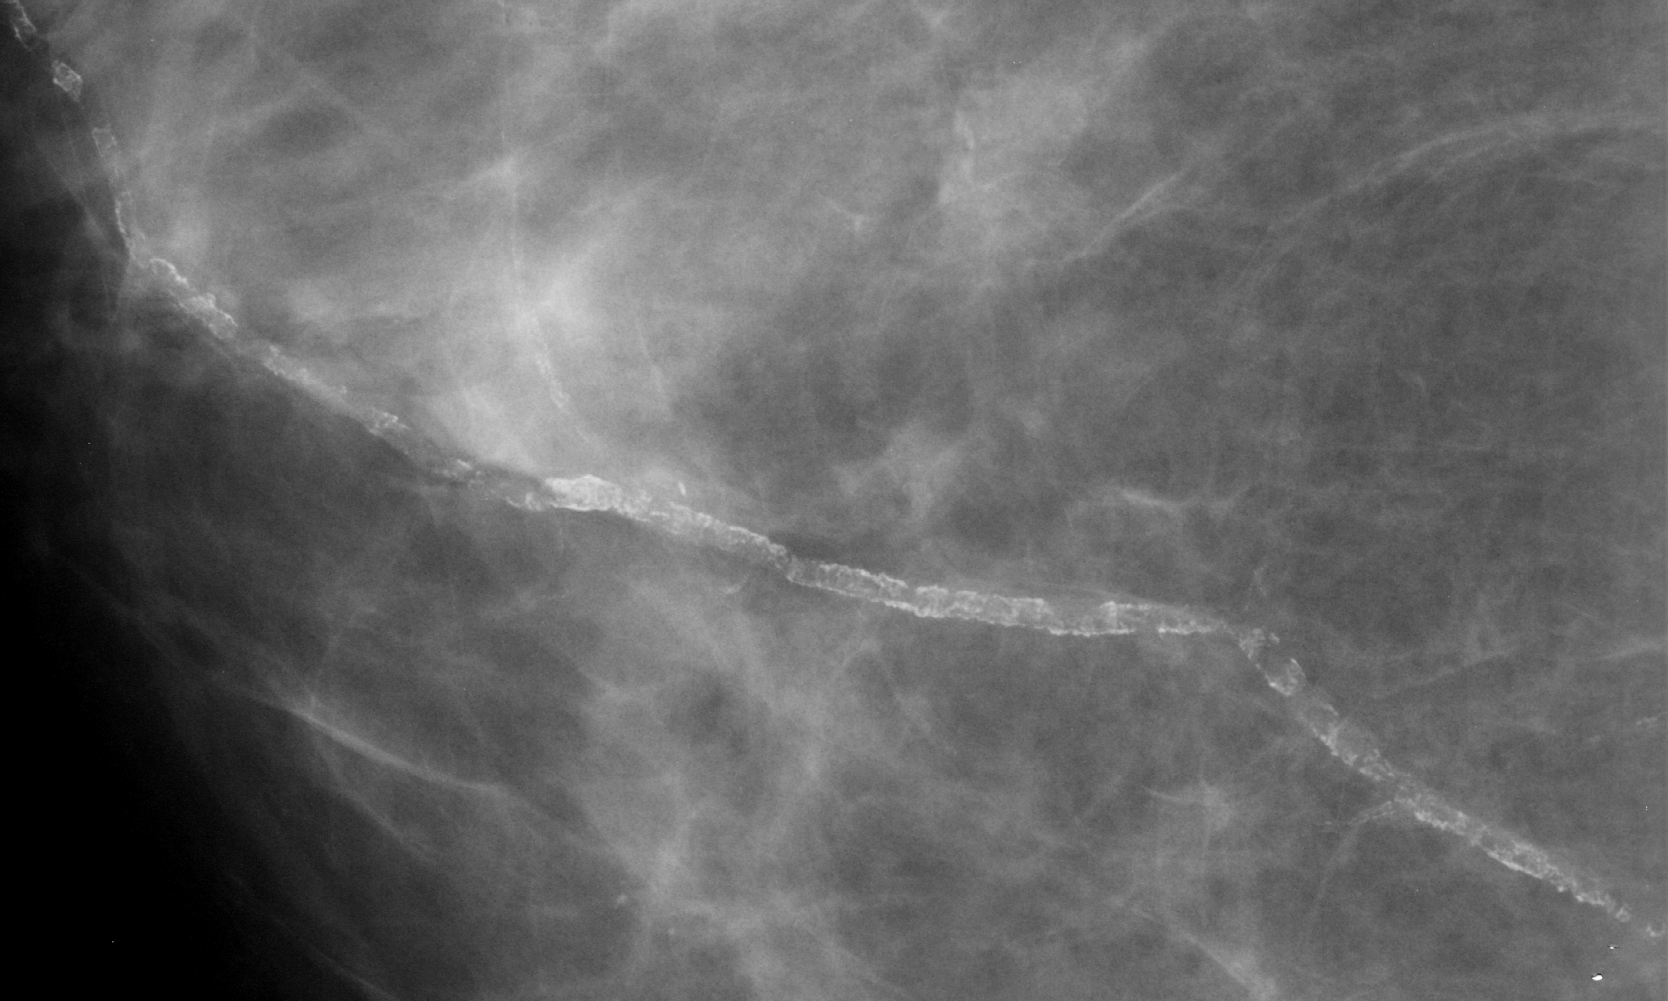
Region of interest cut from a scanned film mammogram (one marked finding), right breast, CC view.
Calcifications, morphology vascular; BI-RADS assessment category 2; subtlety rating 5 on a 1 (subtle) to 5 (obvious) scale; benign without callback (not worked up further).